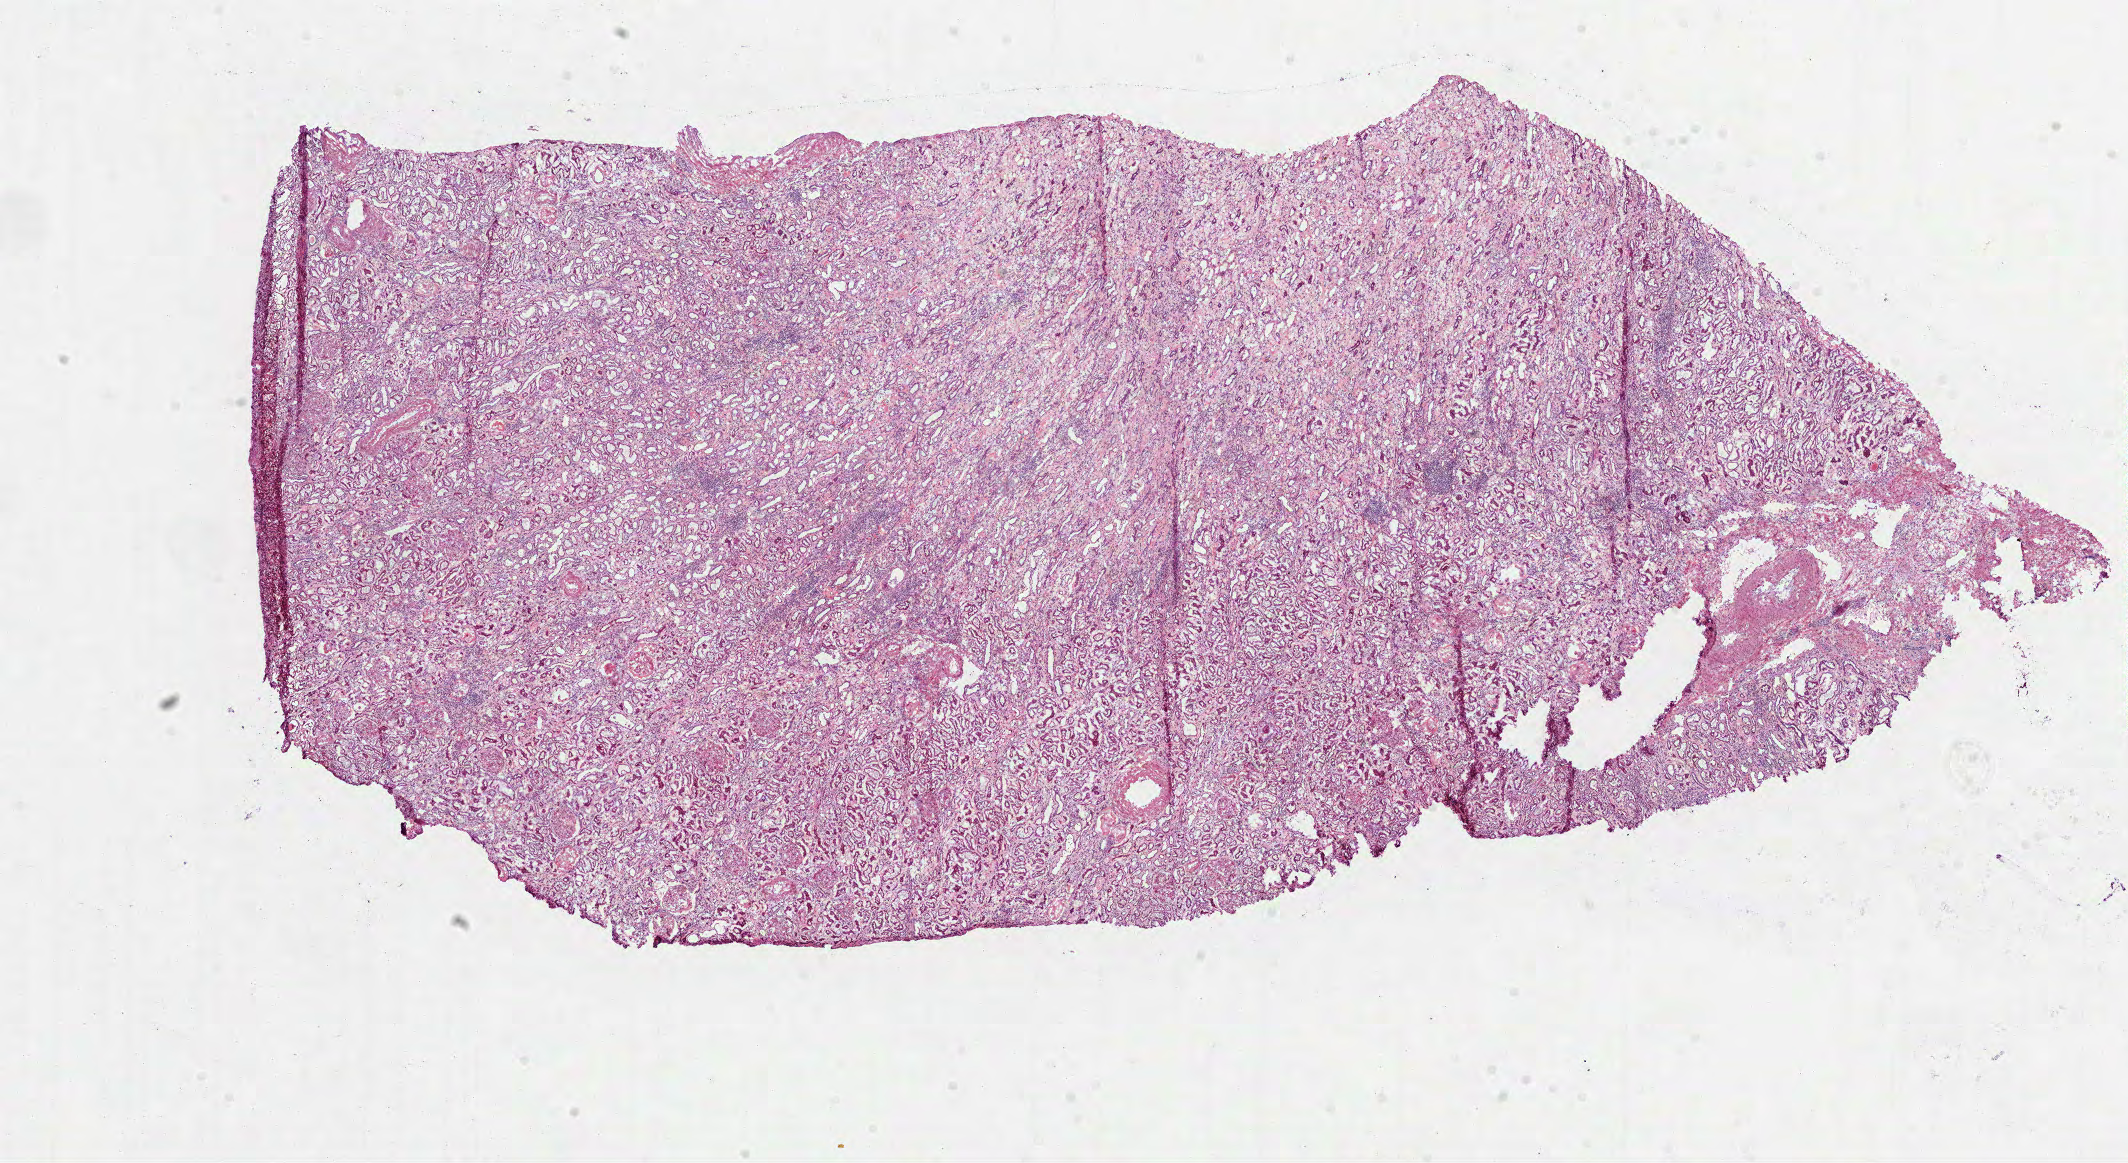
Whole-slide histology image, Hematoxylin and eosin (H&E) stained, shown as a low-resolution overview of the whole scanned area (about 17.2 x 9.4 mm, slide scanned at 40x). Frozen section from the top of the tissue portion. Kidney, solid tissue normal (non-tumour tissue) sample. Male, age 67 years at initial diagnosis.
This section: solid tissue normal (non-tumour) sample from the same patient. Patient diagnosis: Papillary adenocarcinoma, NOS.